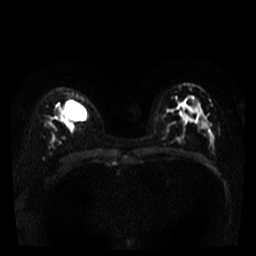
Breast MRI, one axial slice; position 26 of 40 along the scan axis; diffusion-weighted series; image 2 of 4 stored at this slice position (different b-values; order by instance number); 3 T; 5 mm slice thickness; 256 × 256 image matrix. Female patient.
Outlined on this slice (expert manual segmentation):
- tumour on diffusion-weighted imaging: bounding box [x1, y1, x2, y2] px = [66, 101, 86, 120]